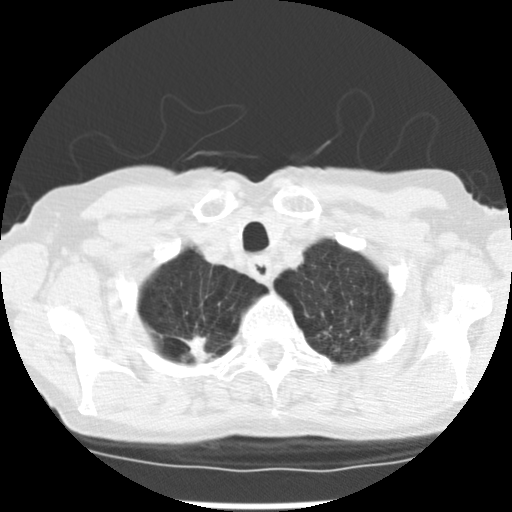
Low-dose screening chest CT, axial slice; baseline screening round; lung window (W 1500 / L -600 HU); standard (soft-tissue) reconstruction kernel (STANDARD); slice 22 of 265 in the series; 512 × 512 image matrix, field of view 300 × 300 mm. Female, age 72 years at enrolment. Current smoker at enrolment.
Expert reader's lesion annotation, box from (x=167, y=317) to (x=231, y=364) px. The screening reader recorded 3 non-calcified nodules or masses ≥4 mm on this exam; which of them this box marks is not recorded. Lung cancer was diagnosed 50 days after this screen: adenocarcinoma, NOS, right upper lobe, moderately differentiated (G2), stage IB (AJCC 6th edition), 22 mm at pathology.